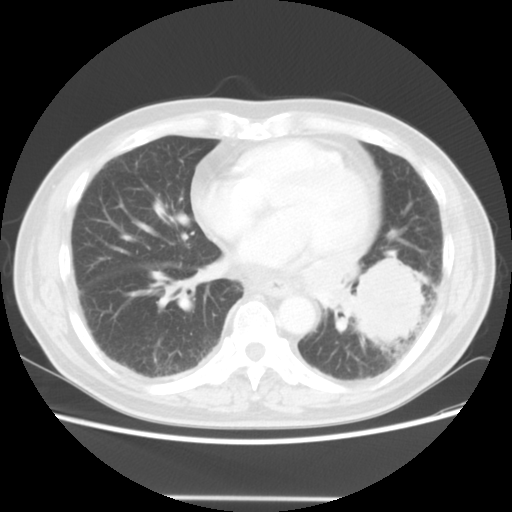
Chest CT, one axial slice. Slice 19 of 56 in the series (ordered by position). Reconstruction kernel STANDARD. 140 kVp. Lung window (W 1500 / L -600 HU). 5 mm slice thickness. 512 × 512 image matrix. Male patient, age 66 years. From the clinical record (not read from this slice): clinical TNM (as recorded): T4 N3 M0; histopathological grade: G3.
Annotated regions visible in this slice (rectangle marked by the reading radiologist):
- lung tumour (recorded histology: small cell carcinoma): box from (x=347, y=248) to (x=427, y=345) px